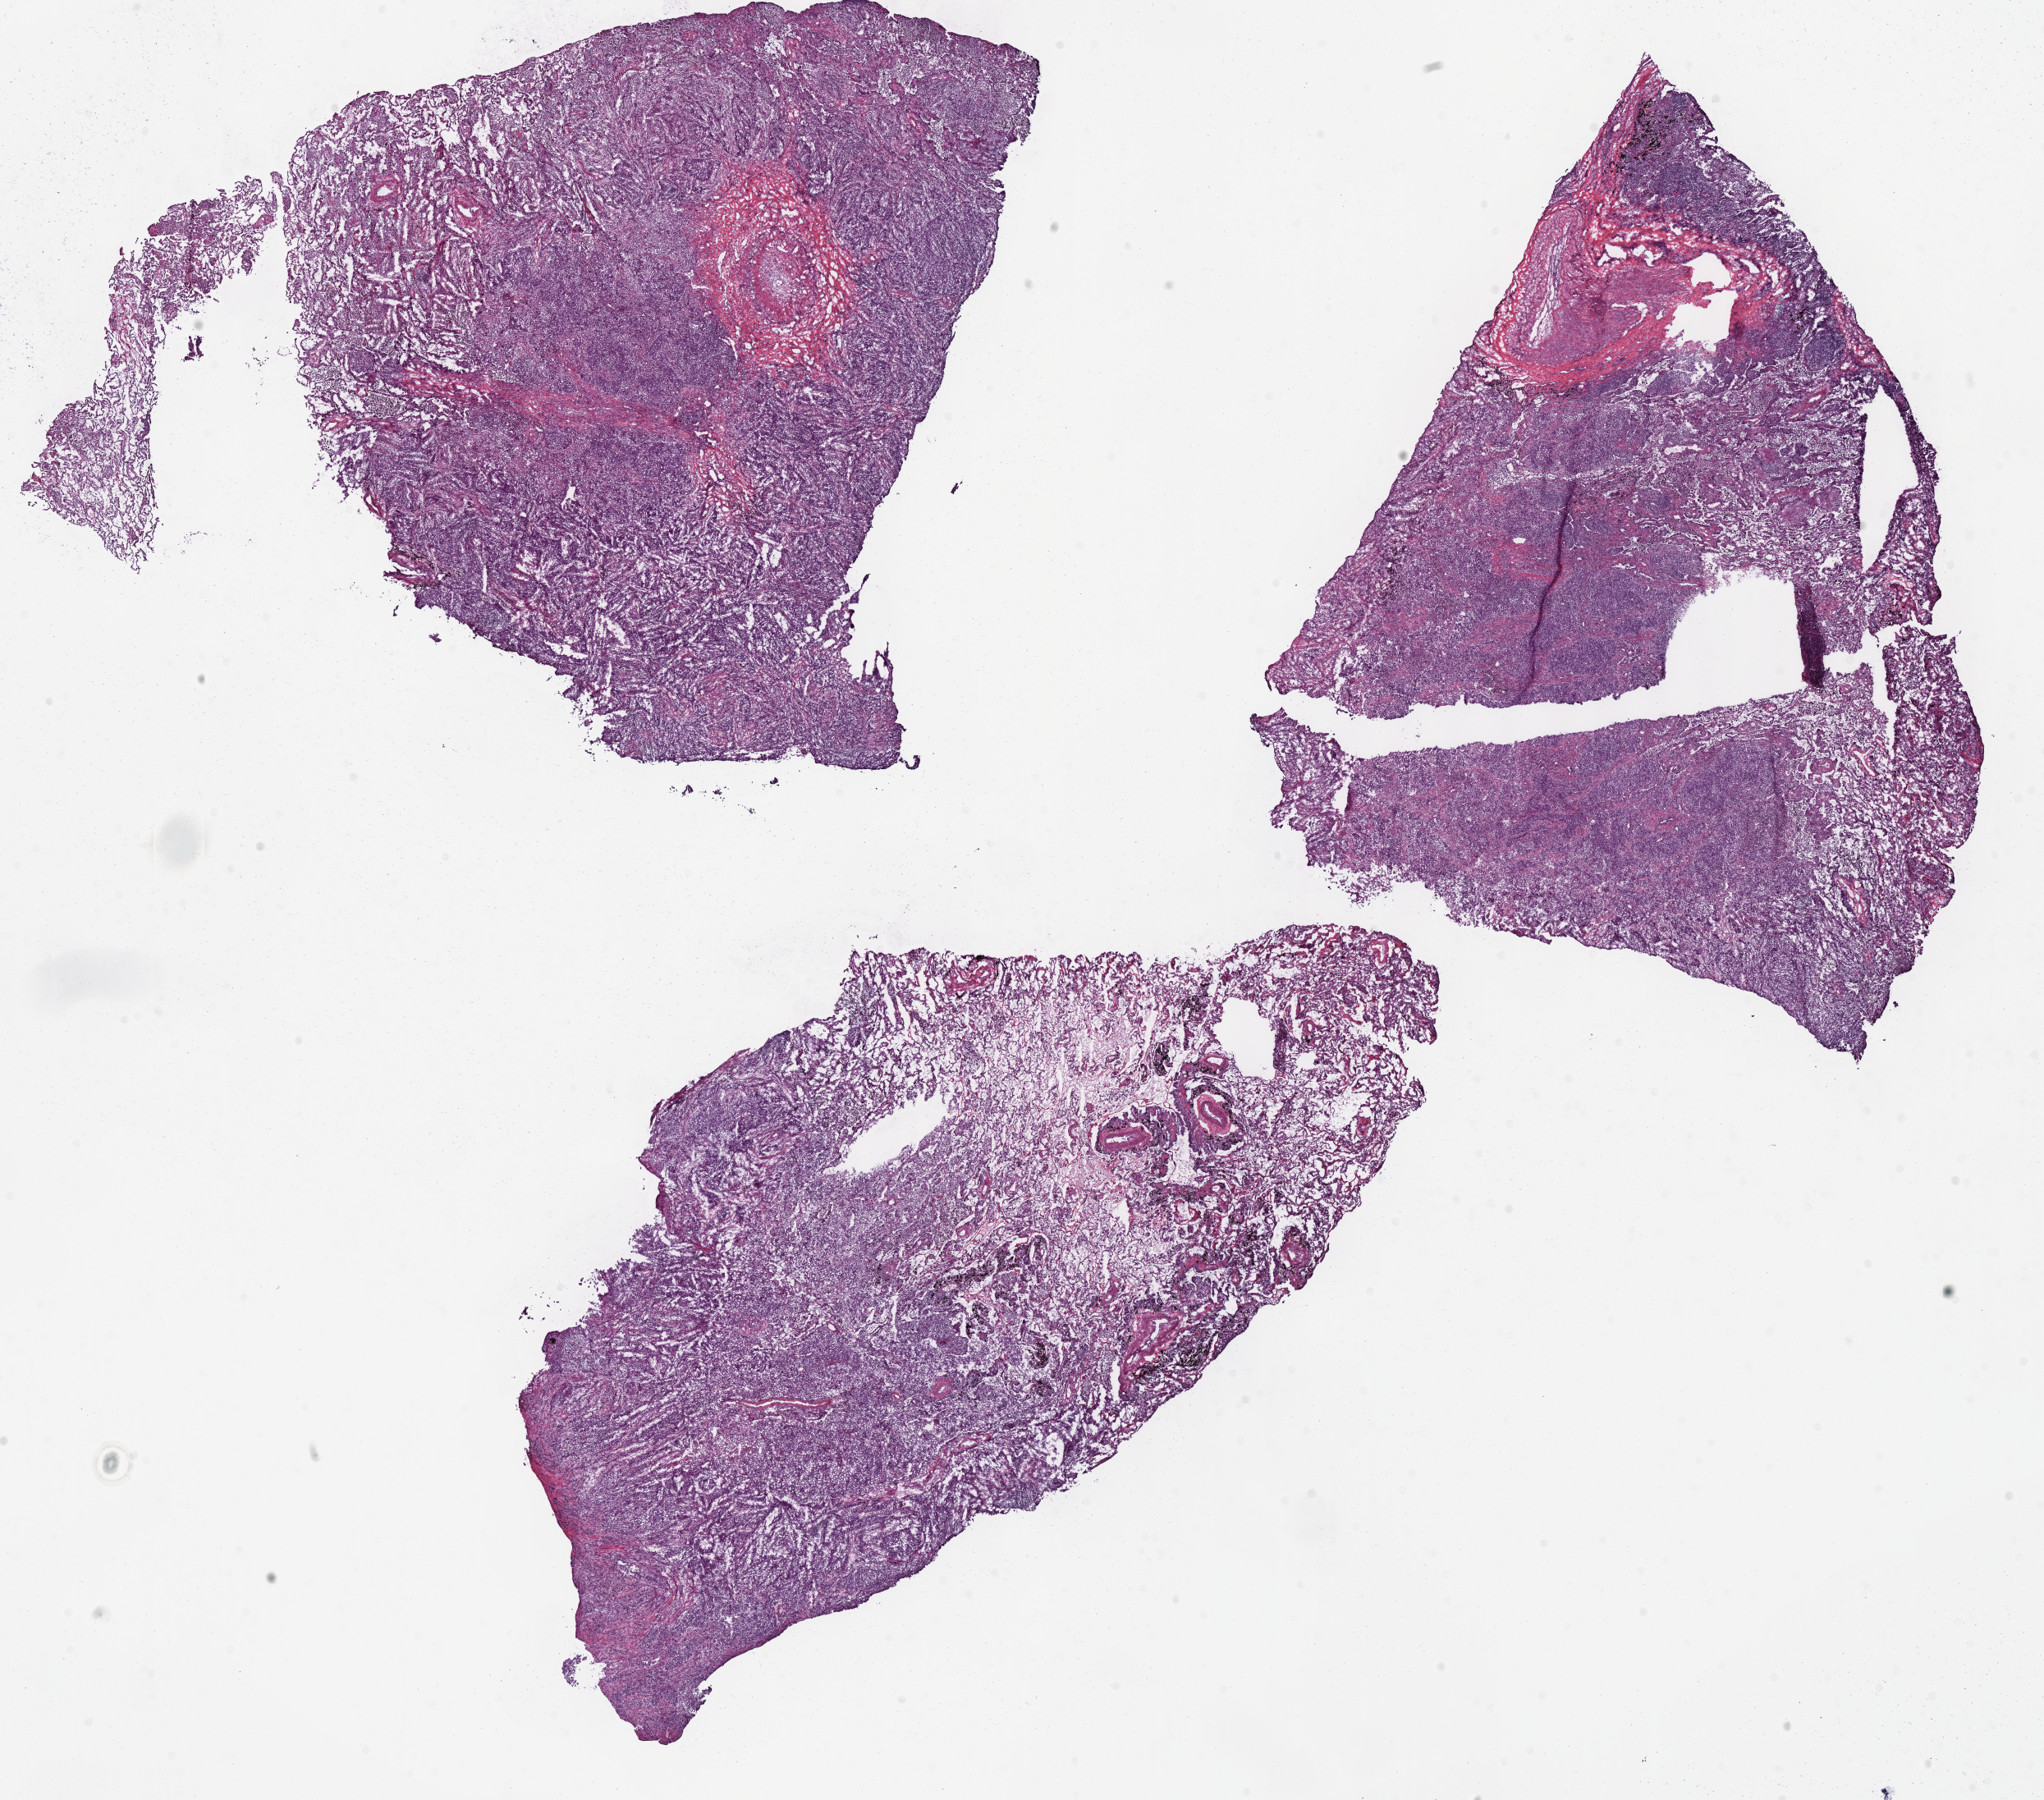
Whole-slide histology image, Hematoxylin and eosin (H&E) stained — a low-resolution overview of the entire scanned area, about 19.6 x 17.2 mm (slide scanned at 40x), frozen section from the bottom of the tissue portion, lung, primary tumour sample. Male, age 62 years at initial diagnosis. Composition of this section per pathologist review: tumour cells 60%, tumour nuclei 65%, normal cells 3%, stromal cells 33%, necrosis 4%. Infiltration values recorded for this section: lymphocyte infiltration 20%, monocyte infiltration 5%, neutrophil infiltration 2%.
- AJCC pathologic stage: IA
- laterality: left
- diagnosis: Squamous cell carcinoma, NOS (lower lobe, lung)